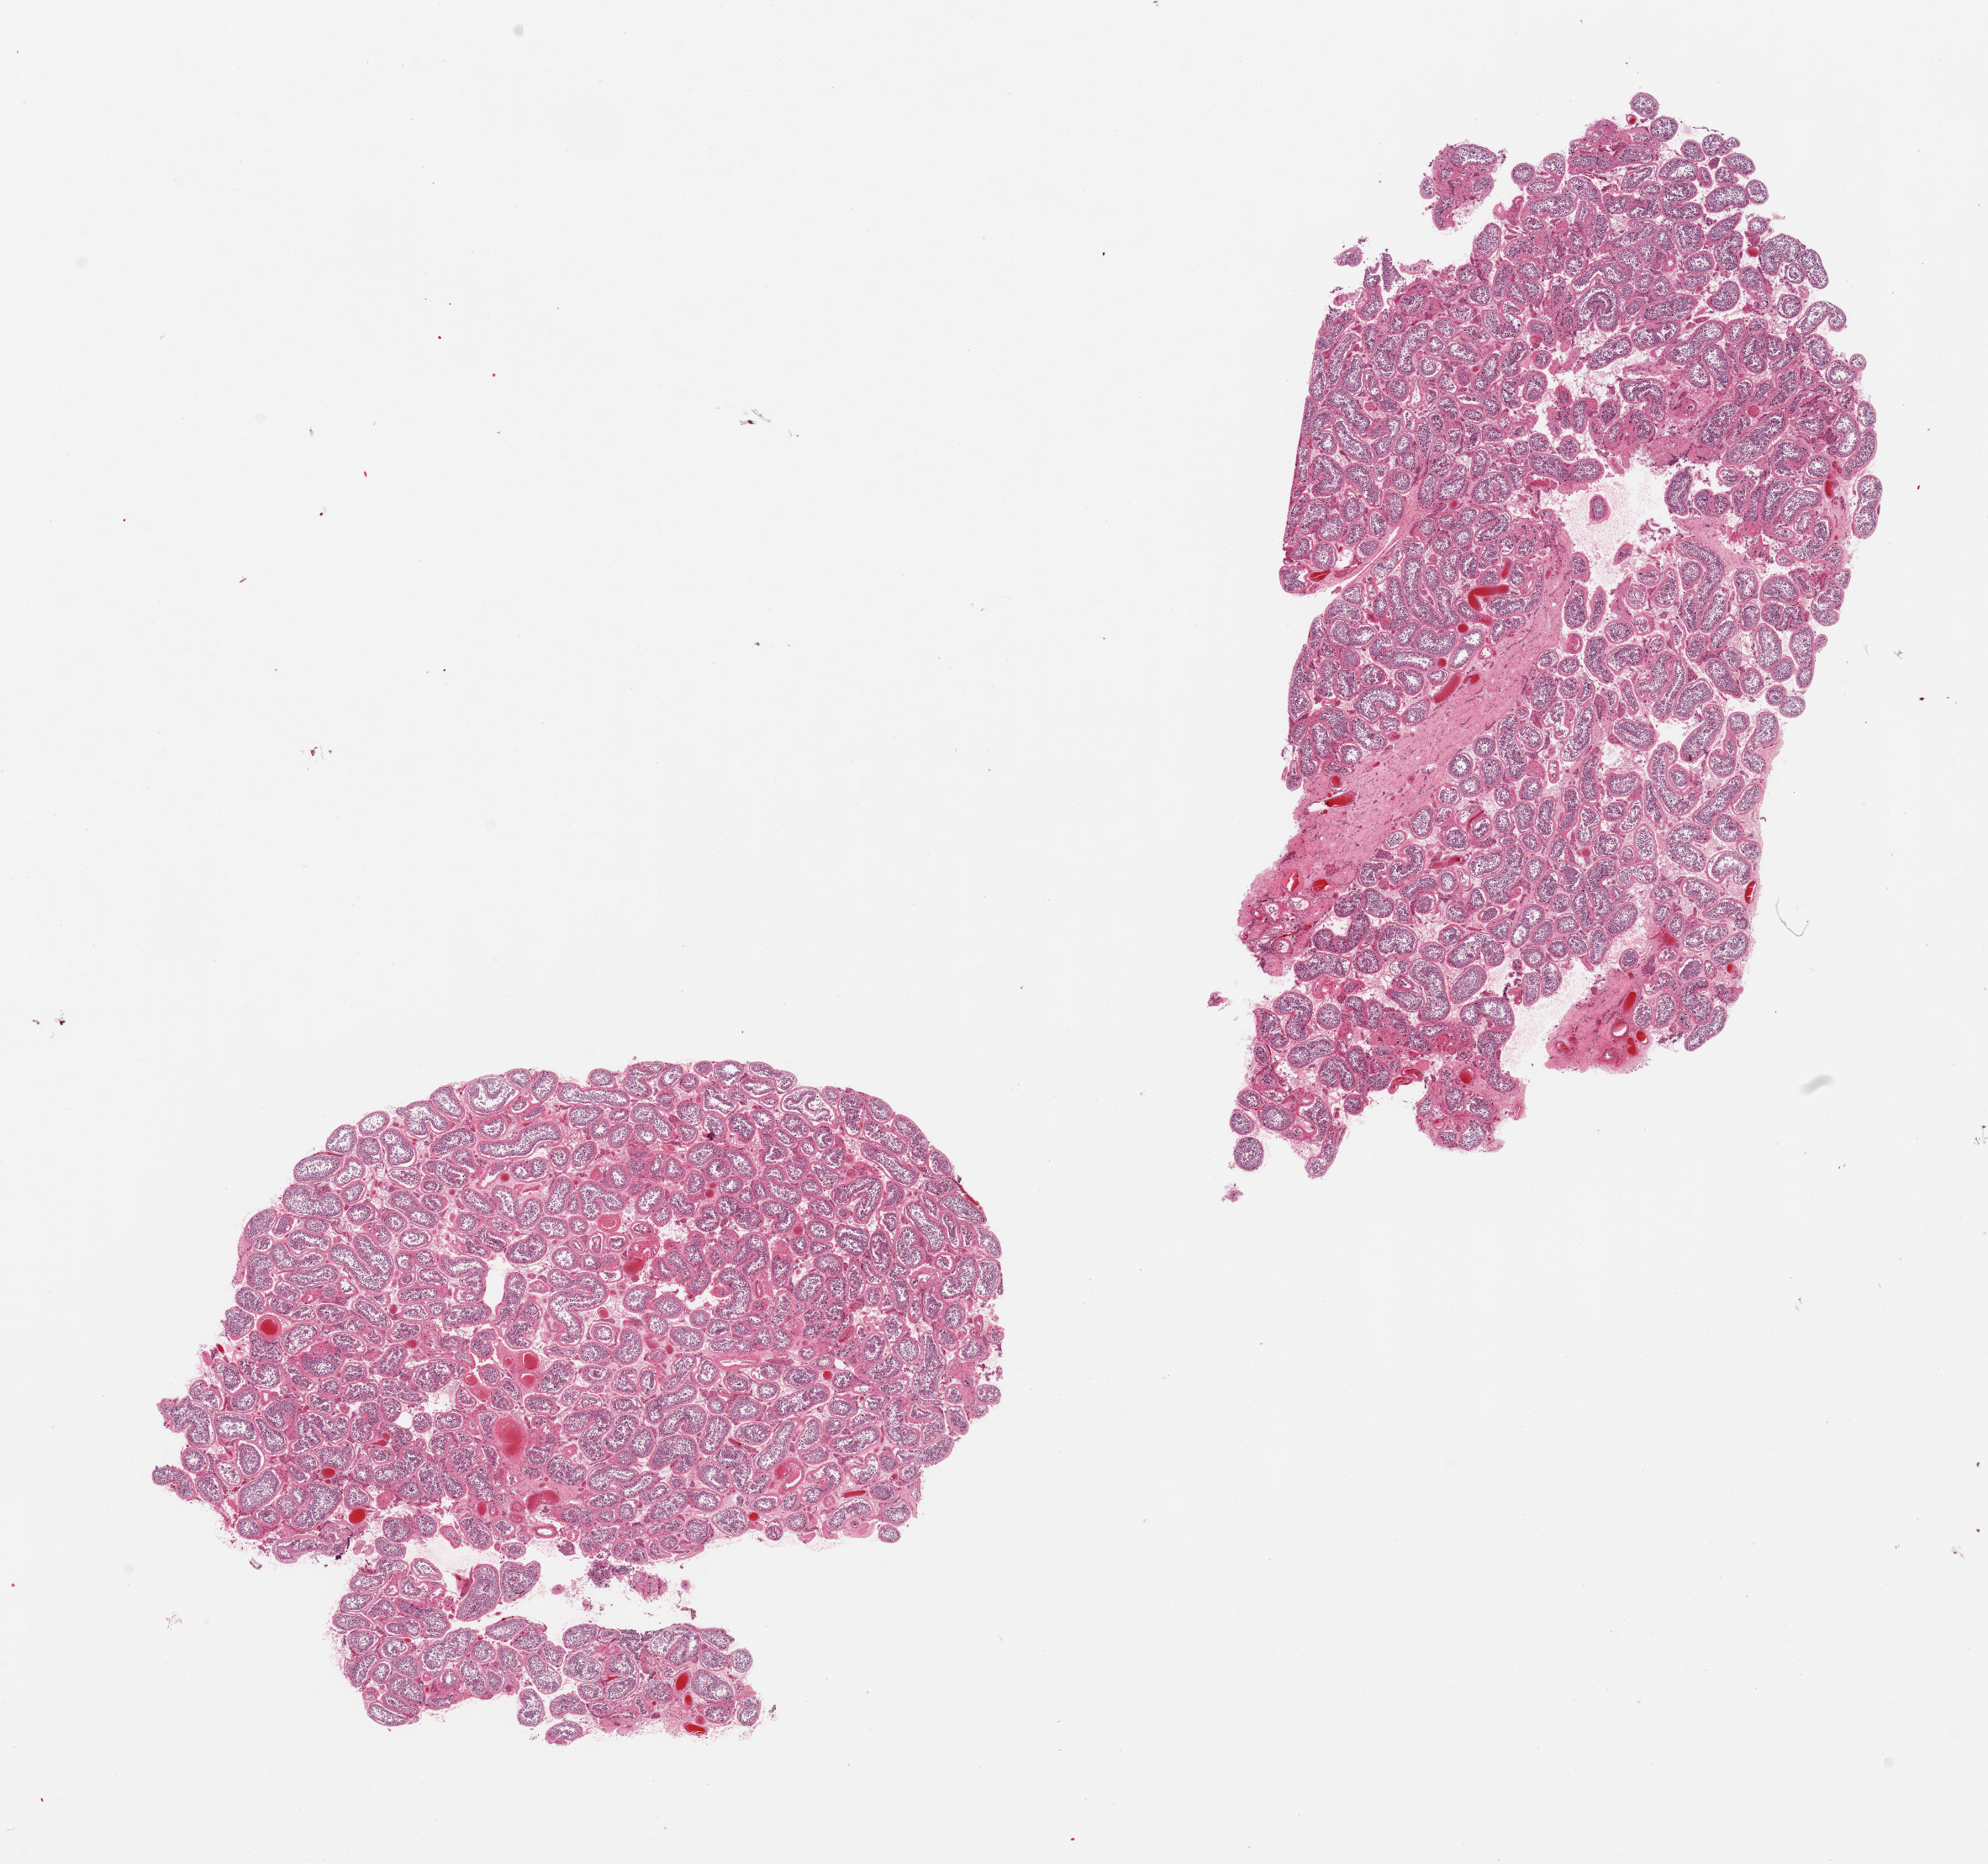
Haematoxylin and eosin whole-slide image — a low-resolution overview of the entire scanned area, about 18.7 x 17.5 mm, PAXgene-fixed paraffin-embedded (PFPE) section, section of testis (target tissue), donor tissue sample. Donor: male.
- review note (as recorded): 2 pieces, active spermatogenesis